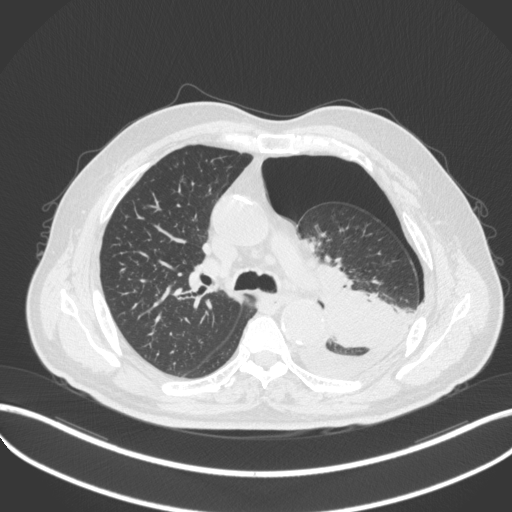
Chest CT, one axial slice. Position 336 of 466 along the scan axis. Reconstruction kernel B31f. 120 kVp. Lung window (W 1500 / L -600 HU). 1 mm slice thickness. 512 × 512 image matrix. Patient: male, 76 years. From the clinical record (not read from this slice): clinical TNM (as recorded): T3 N0 M1b.
Annotated regions visible in this slice (rectangle marked by the reading radiologist):
- lung tumour (recorded histology: adenocarcinoma): bounding box <288,286,410,380> (left, top, right, bottom; pixels)